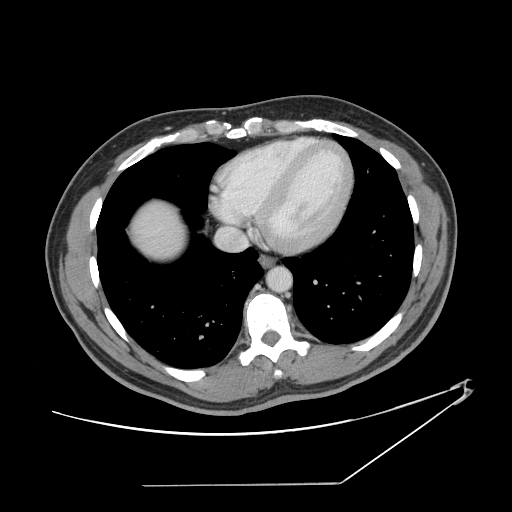
Contrast-enhanced abdominal CT, one axial slice; position 140 of 152 along the scan axis; reconstruction kernel STANDARD; 120 kVp; intravenous contrast given; soft-tissue window (W 400 / L 40 HU); 2.5 mm slice thickness; 512 × 512 image matrix, field of view 432 × 432 mm. Male patient, age 45 years. Case-level facts recorded for this patient, not image findings: diagnosis: colorectal cancer liver metastases, imaged before liver resection; multiple liver metastases: no; largest metastasis: 1 cm; disease in both lobes: no.
Outlined on this slice (expert manual segmentation):
- hepatic veins: bounding box [x1, y1, x2, y2] px = [230, 229, 248, 247]
- liver: [137, 203, 183, 256]
- planned liver remnant (the part of the liver to remain after resection): [136, 202, 183, 256]